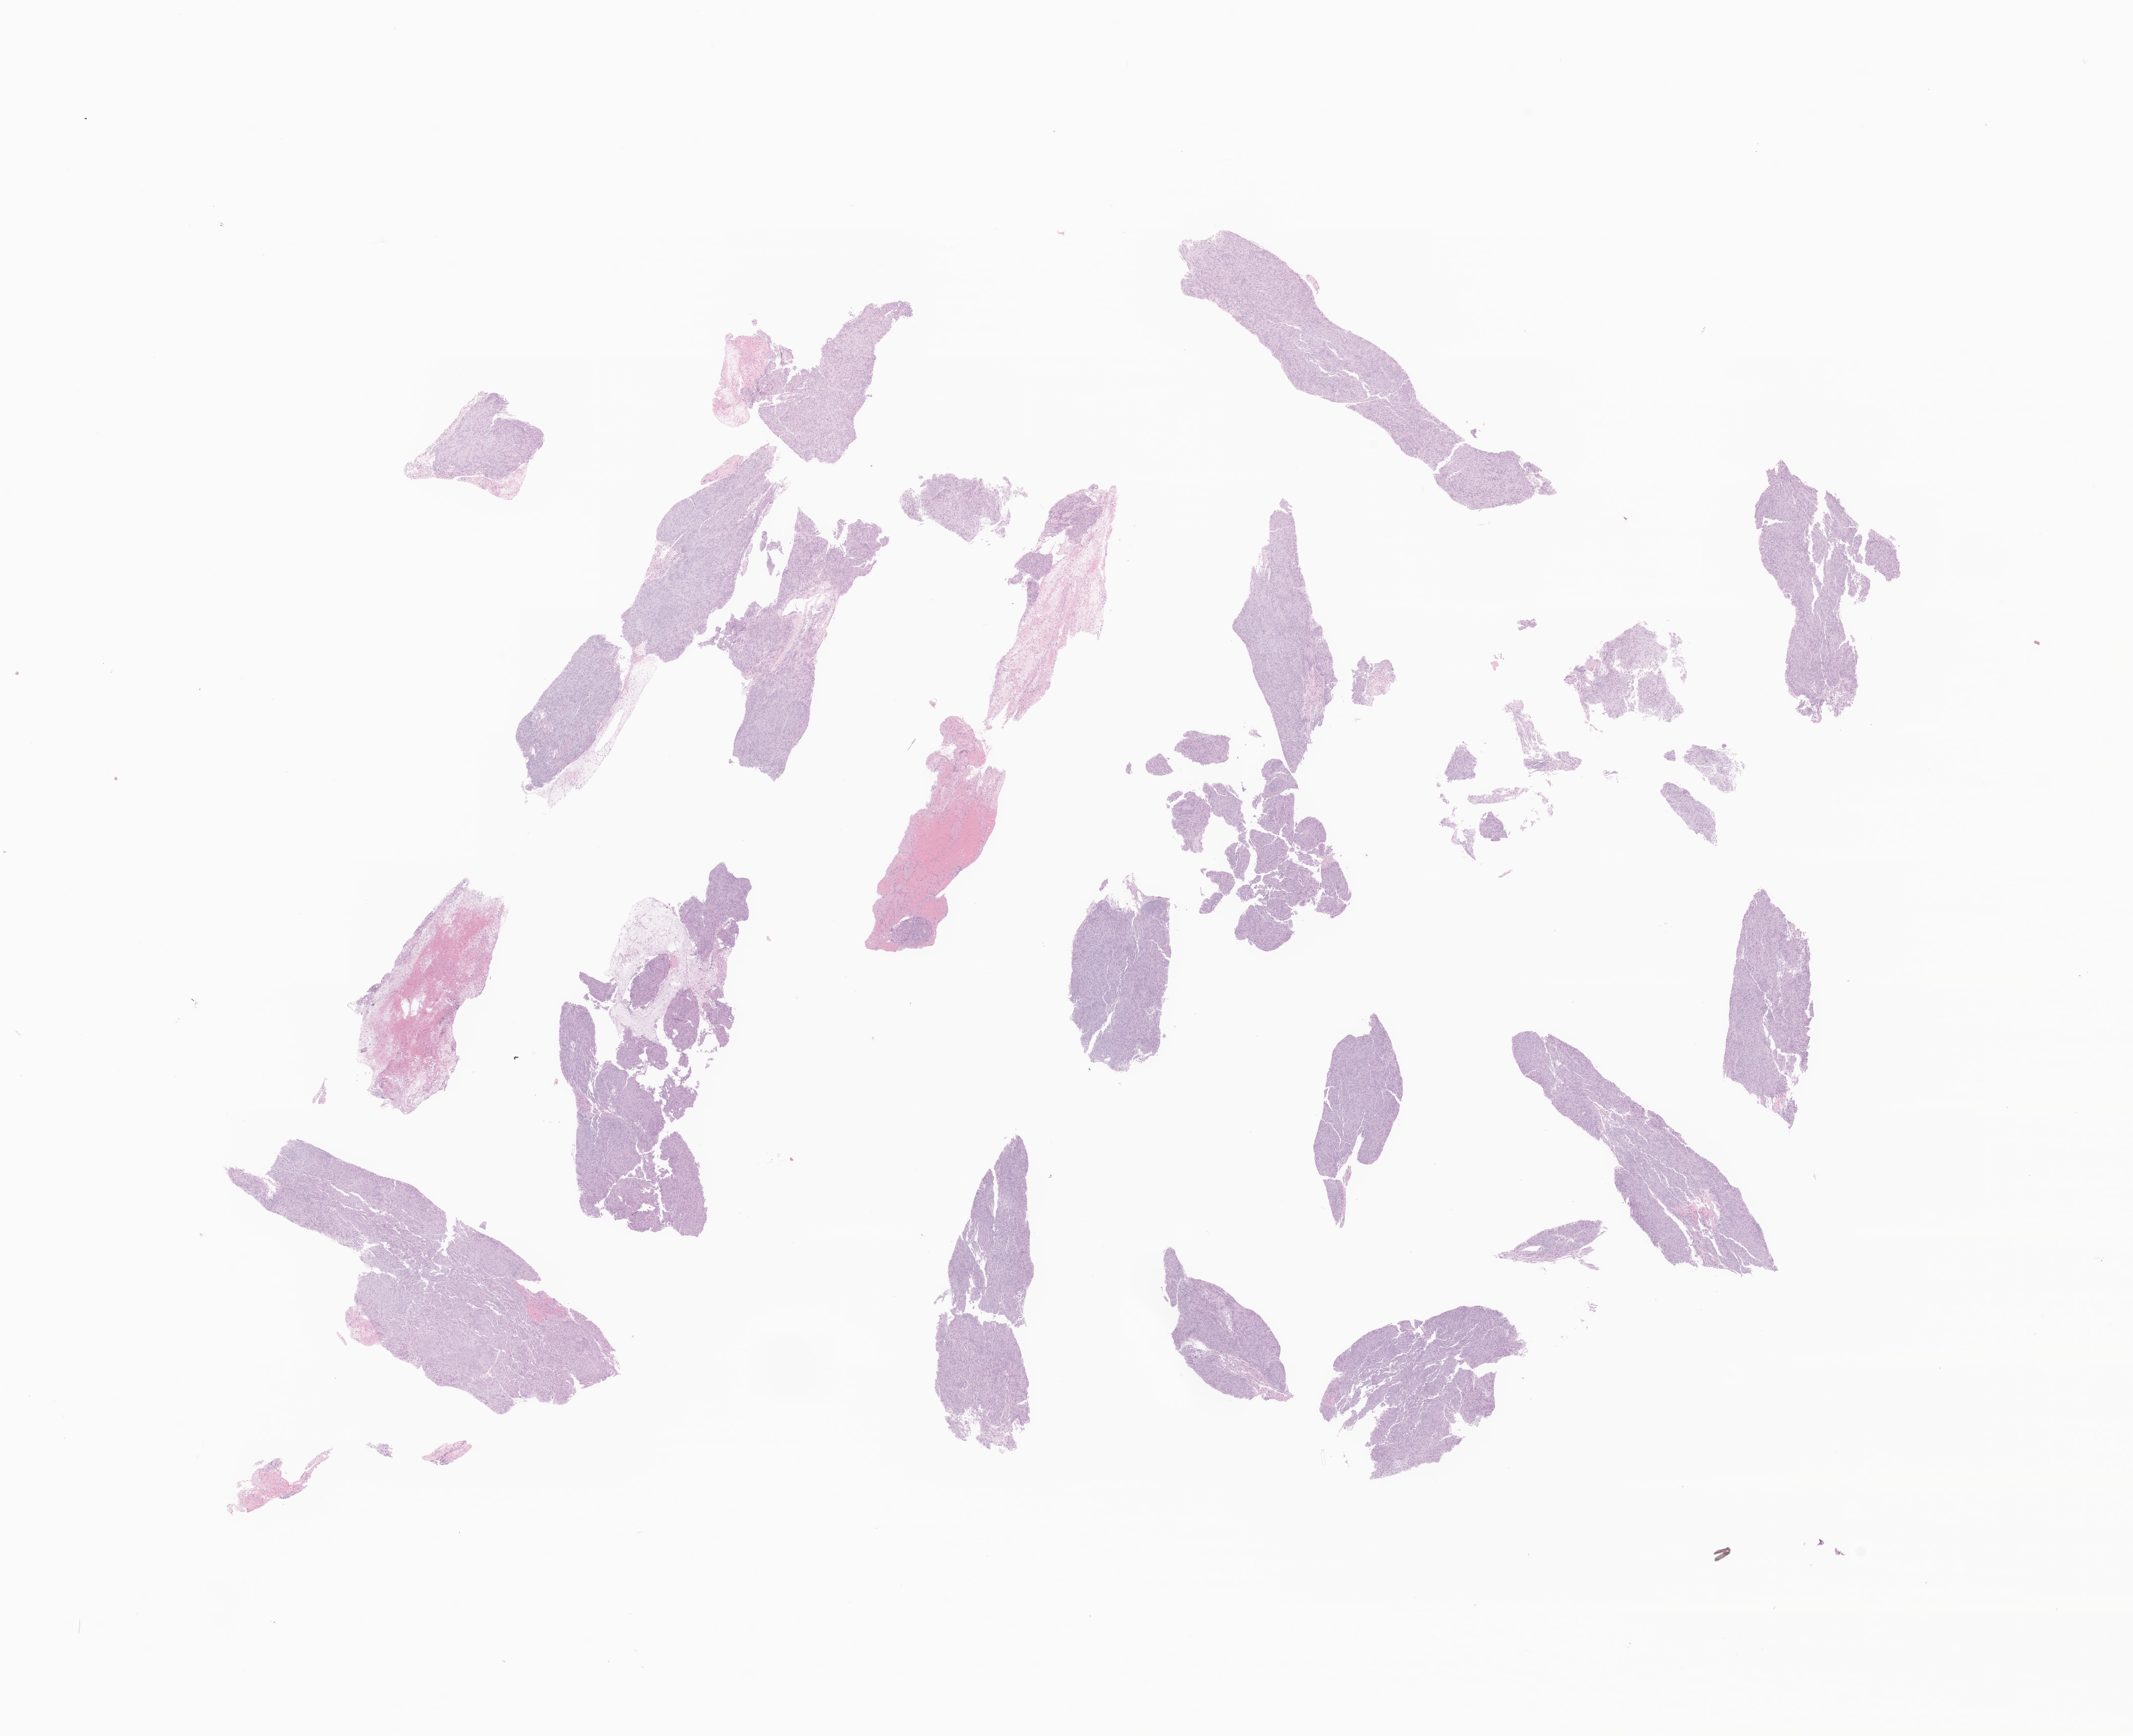
Whole-slide image, H&E stain of tumor tissue from the abdomen — whole scanned area (about 18.1 x 14.8 mm) shown as a low-resolution overview. Patient sex: female.
Specimen: formalin-fixed, paraffin-embedded (FFPE) tissue.